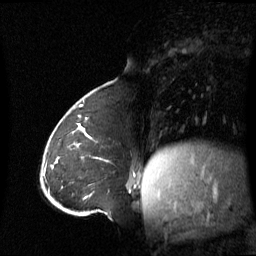
Breast MRI (dynamic contrast-enhanced), one sagittal slice; slice 21 of 60 in the series (ordered by position); dynamic contrast-enhanced series, image 2 of 3 at this slice position (ordered by acquisition); 1.5 T; TE 4.2 ms, TR 8.4 ms; 2.8 mm slice thickness; 256 × 256 image matrix, field of view 270 × 270 mm. Female patient, age 43 years. Case-level facts recorded for this patient, not image findings: setting: breast cancer imaged before/during neoadjuvant chemotherapy; receptor status: triple-negative.
Outlined on this slice (semi-automatic segmentation, software-assisted and operator-edited):
- analysis volume of interest (the breast-tissue region the enhancement analysis was run in; not a lesion): bounding box <62,124,135,180> (left, top, right, bottom; pixels)
- tumour enhancement mask (voxels above the 70 % enhancement threshold inside the analysis volume of interest): <72,132,135,175>